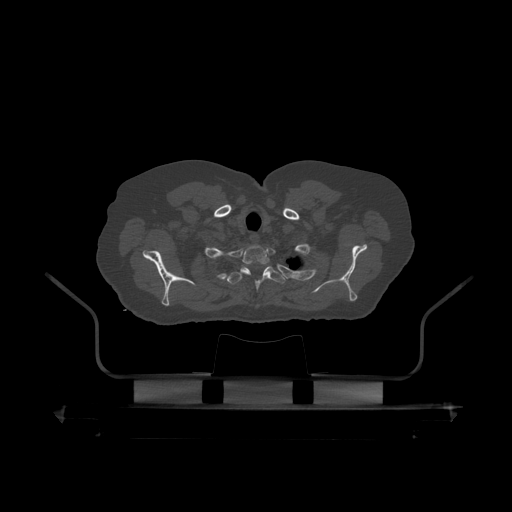
CT including the spine, one axial slice; slice 383 of 390 in the series (ordered by position); reconstruction kernel STANDARD; 120 kVp; bone window (W 1800 / L 400 HU); 1.25 mm slice thickness; 512 × 512 image matrix, field of view 650 × 650 mm. Patient: male, 60 years. Case-level facts recorded for this patient, not image findings: primary cancer: prostate.
Outlined on this slice (semi-automatic segmentation, software-assisted and operator-edited):
- T1 vertebra: box from (x=213, y=245) to (x=271, y=276) px
- T2 vertebra: (x=228, y=266)–(x=286, y=309)